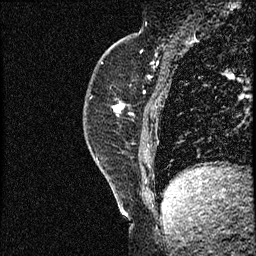
Breast MRI (dynamic contrast-enhanced), one sagittal slice. Position 21 of 56 along the scan axis. Dynamic contrast-enhanced study with each time point stored as its own series, time point 2 of 3 at this slice position (early post-contrast, ordered by acquisition time). 1.5 T. TE 4.2 ms, TR 17.3 ms. 2 mm slice thickness. 256 × 256 image matrix, field of view 200 × 200 mm. Female patient. From the clinical record (not read from this slice): setting: breast cancer imaged before/during neoadjuvant chemotherapy; receptor status: HER2-positive.
Structures marked on this image (semi-automatic segmentation, software-assisted and operator-edited):
- analysis volume of interest (the breast-tissue region the enhancement analysis was run in; not a lesion): bounding box <83,50,155,155> (left, top, right, bottom; pixels)
- tumour enhancement mask (voxels above the 100 % enhancement threshold inside the analysis volume of interest): <114,103,125,113>